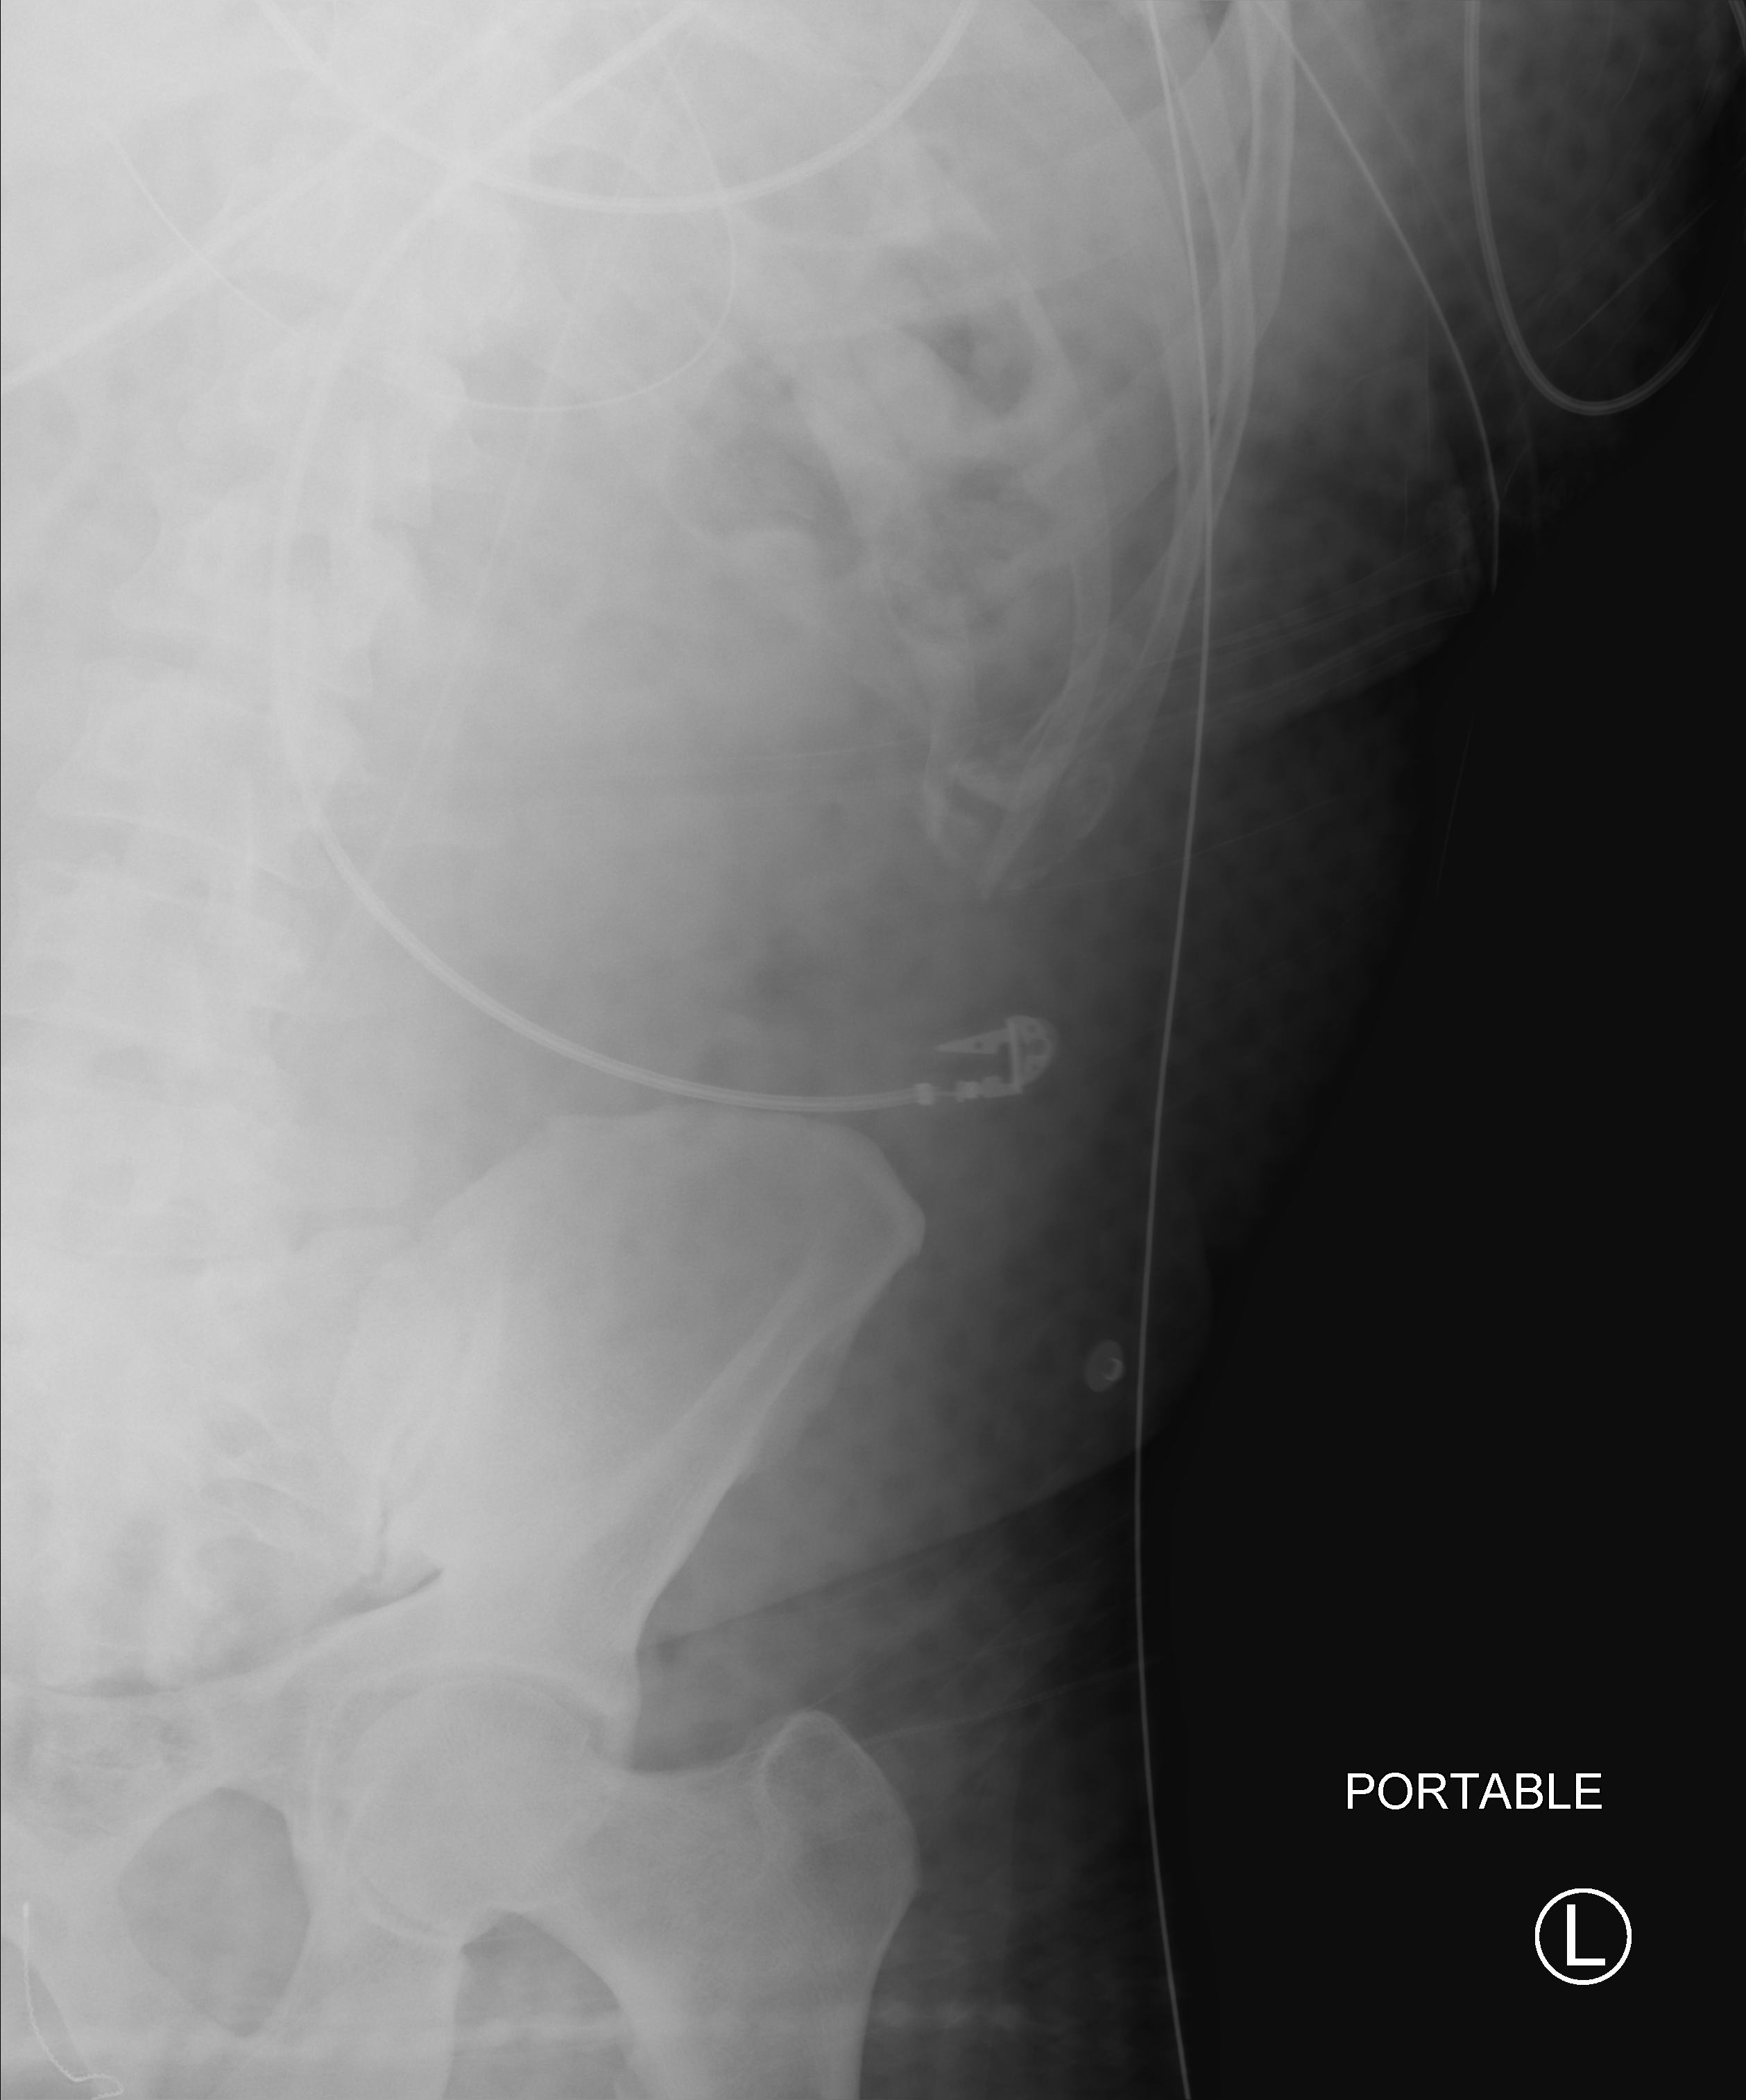
Bedside abdomen radiograph (computed radiography); anteroposterior (AP) projection. Male patient hospitalised with COVID-19, age 18–59 years.
From the hospital-stay record, not from the radiograph (when in the stay this image was taken is not recorded):
- length of hospital stay: 29 days